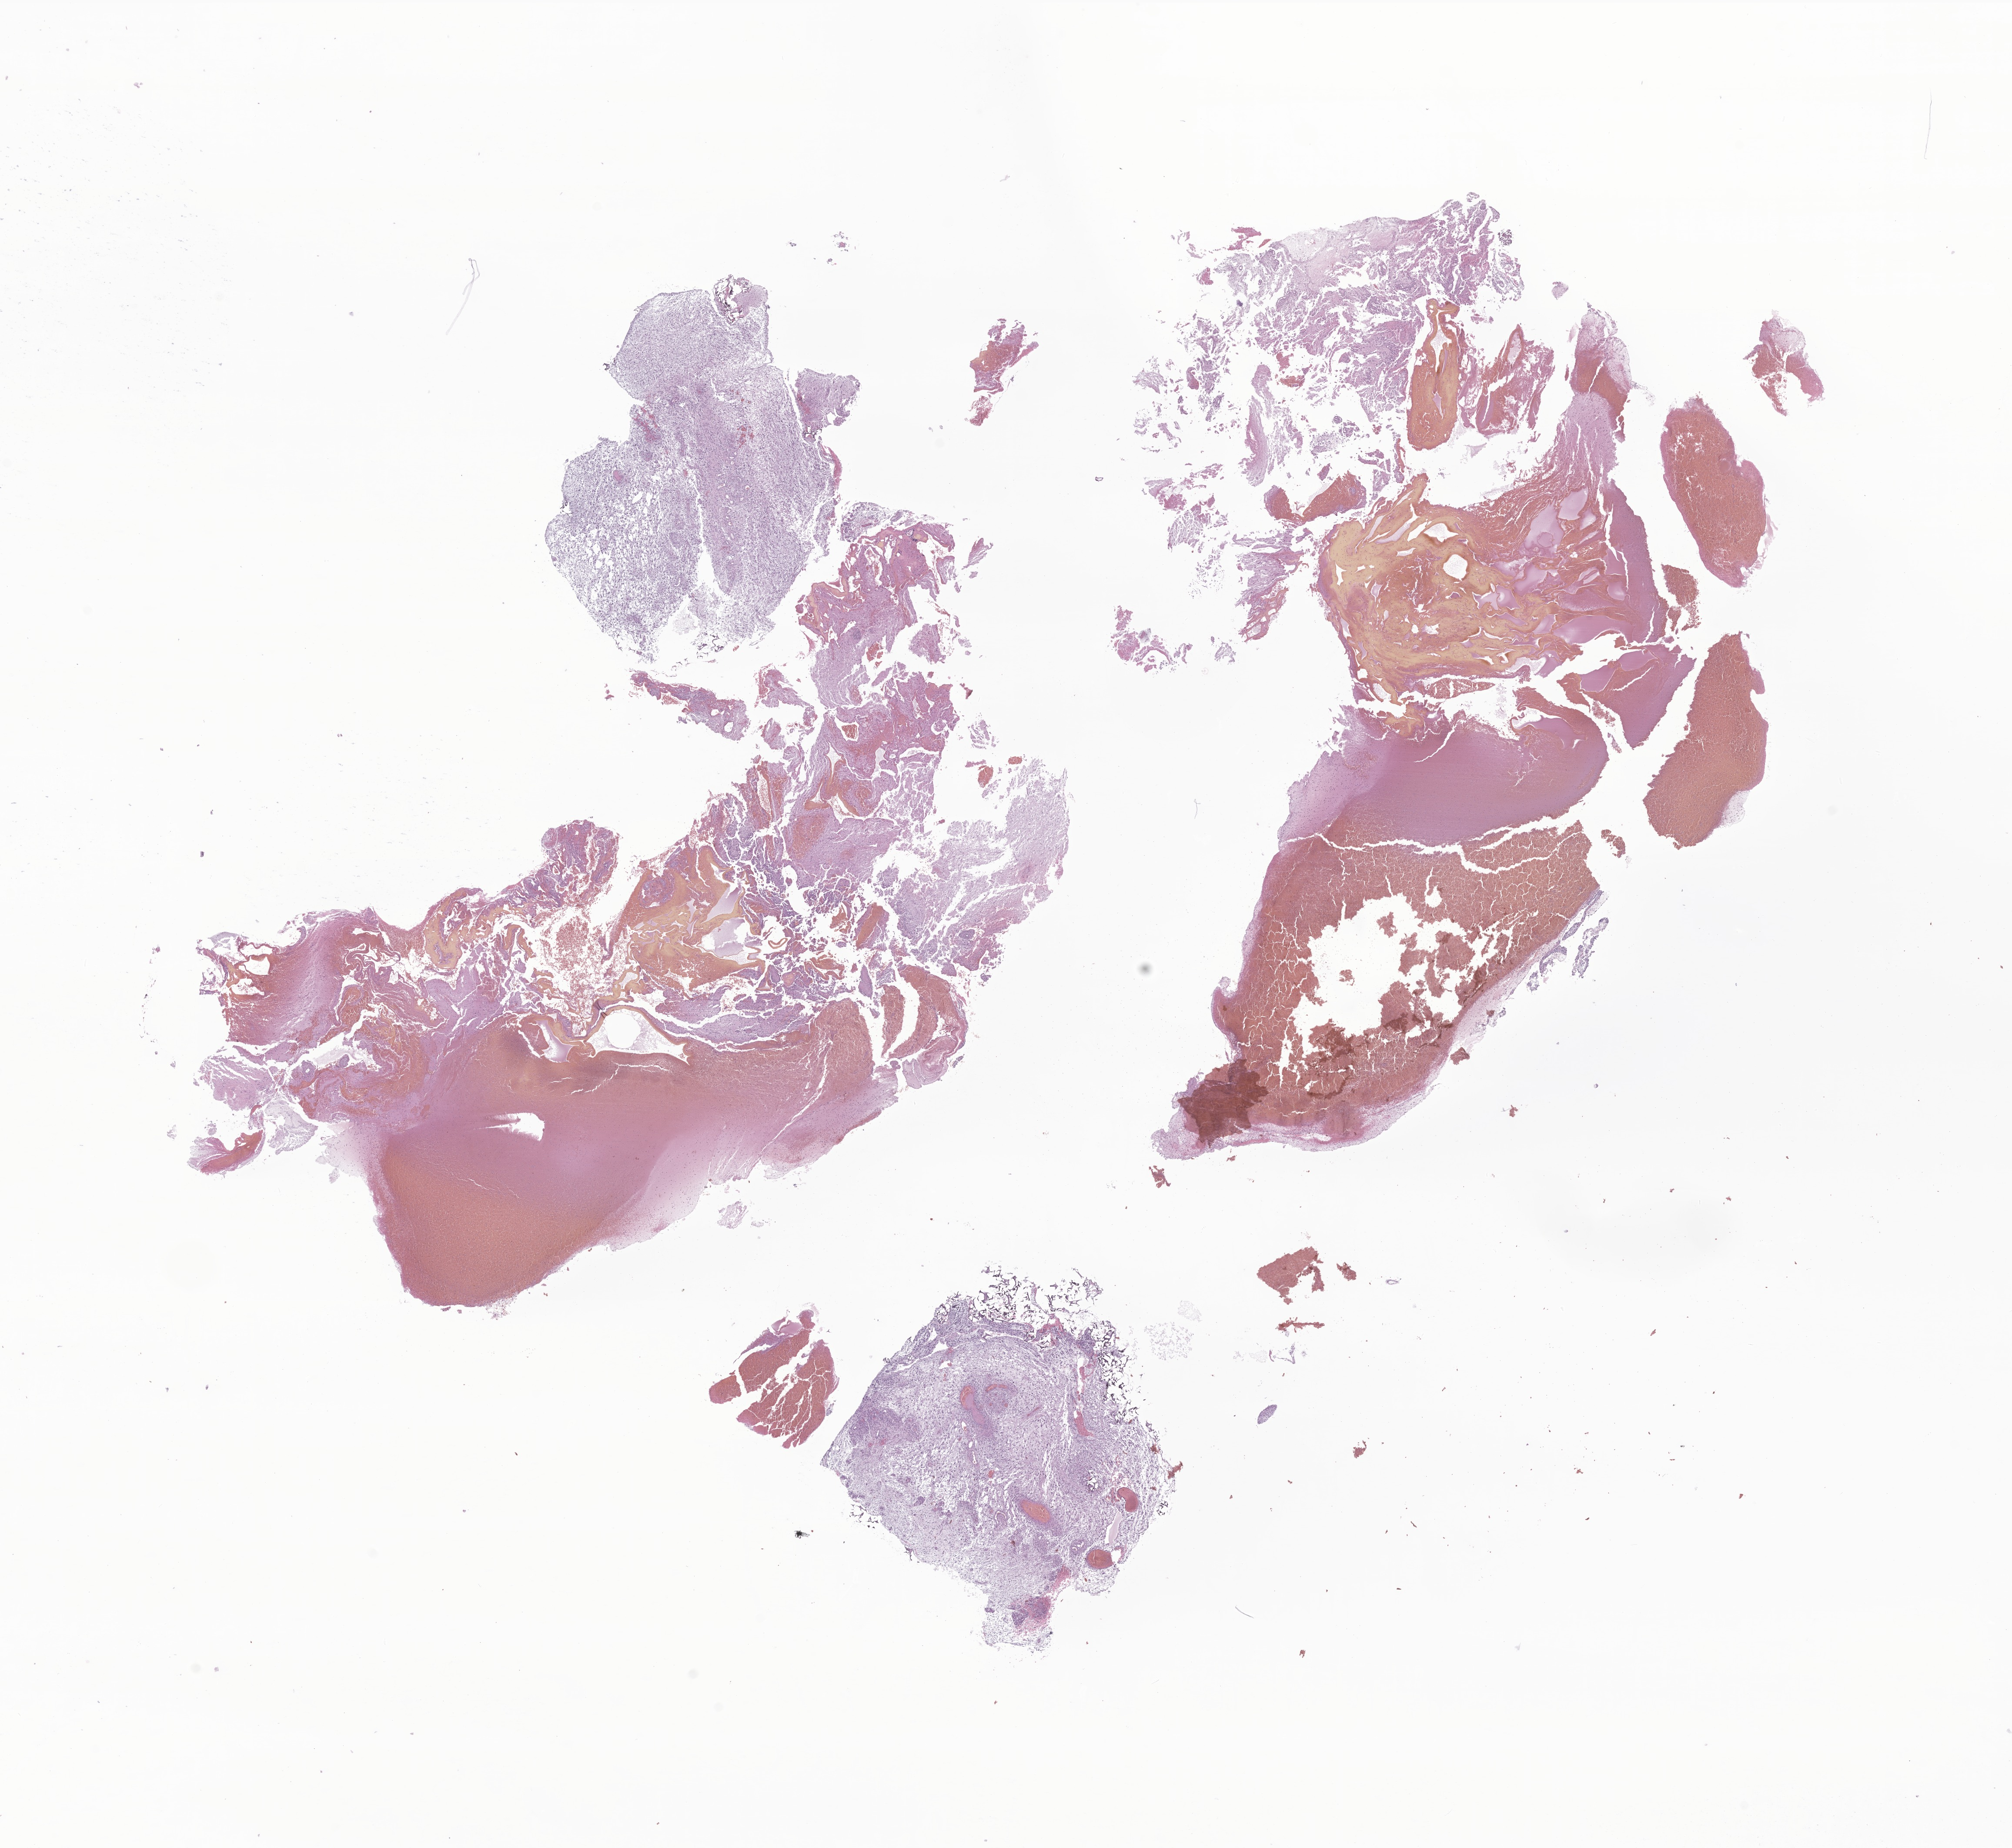
Digitized haematoxylin and eosin-stained section of tumor tissue from the brain, a low-resolution overview of the entire scanned area, about 19.5 x 17.9 mm. FFPE section. Patient: female, age 61 months (5 years 1 month).
Diagnosis: Neoplasm, uncertain whether benign or malignant.